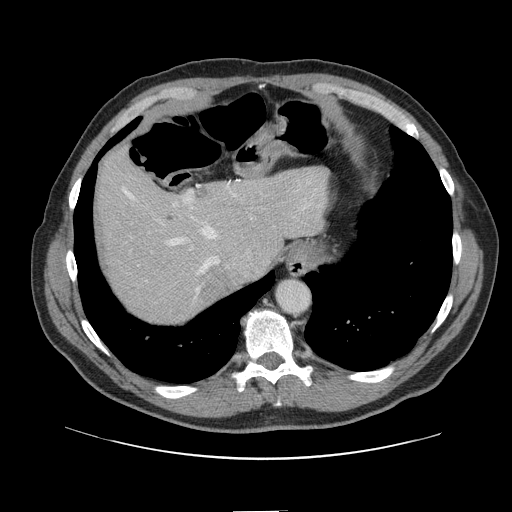
Contrast-enhanced abdominal CT, one axial slice. Slice 116 of 161 in the series (ordered by position). 120 kVp. Intravenous contrast given. Soft-tissue window (W 400 / L 40 HU). 2.5 mm slice thickness. 512 × 512 image matrix. Male patient, age 66 years. From the clinical record (not read from this slice): diagnosis: colorectal cancer liver metastases, imaged before liver resection; multiple liver metastases: no; largest metastasis: 3.5 cm; chemotherapy before resection: yes.
Annotated regions visible in this slice (outlined manually by an expert reader):
- hepatic veins: bounding box [x1, y1, x2, y2] px = [122, 186, 315, 299]
- liver: [99, 151, 325, 320]
- planned liver remnant (the part of the liver to remain after resection): [99, 153, 325, 303]
- portal vein (with intrahepatic branches): [173, 191, 193, 206]
- liver metastasis: [203, 265, 233, 302]